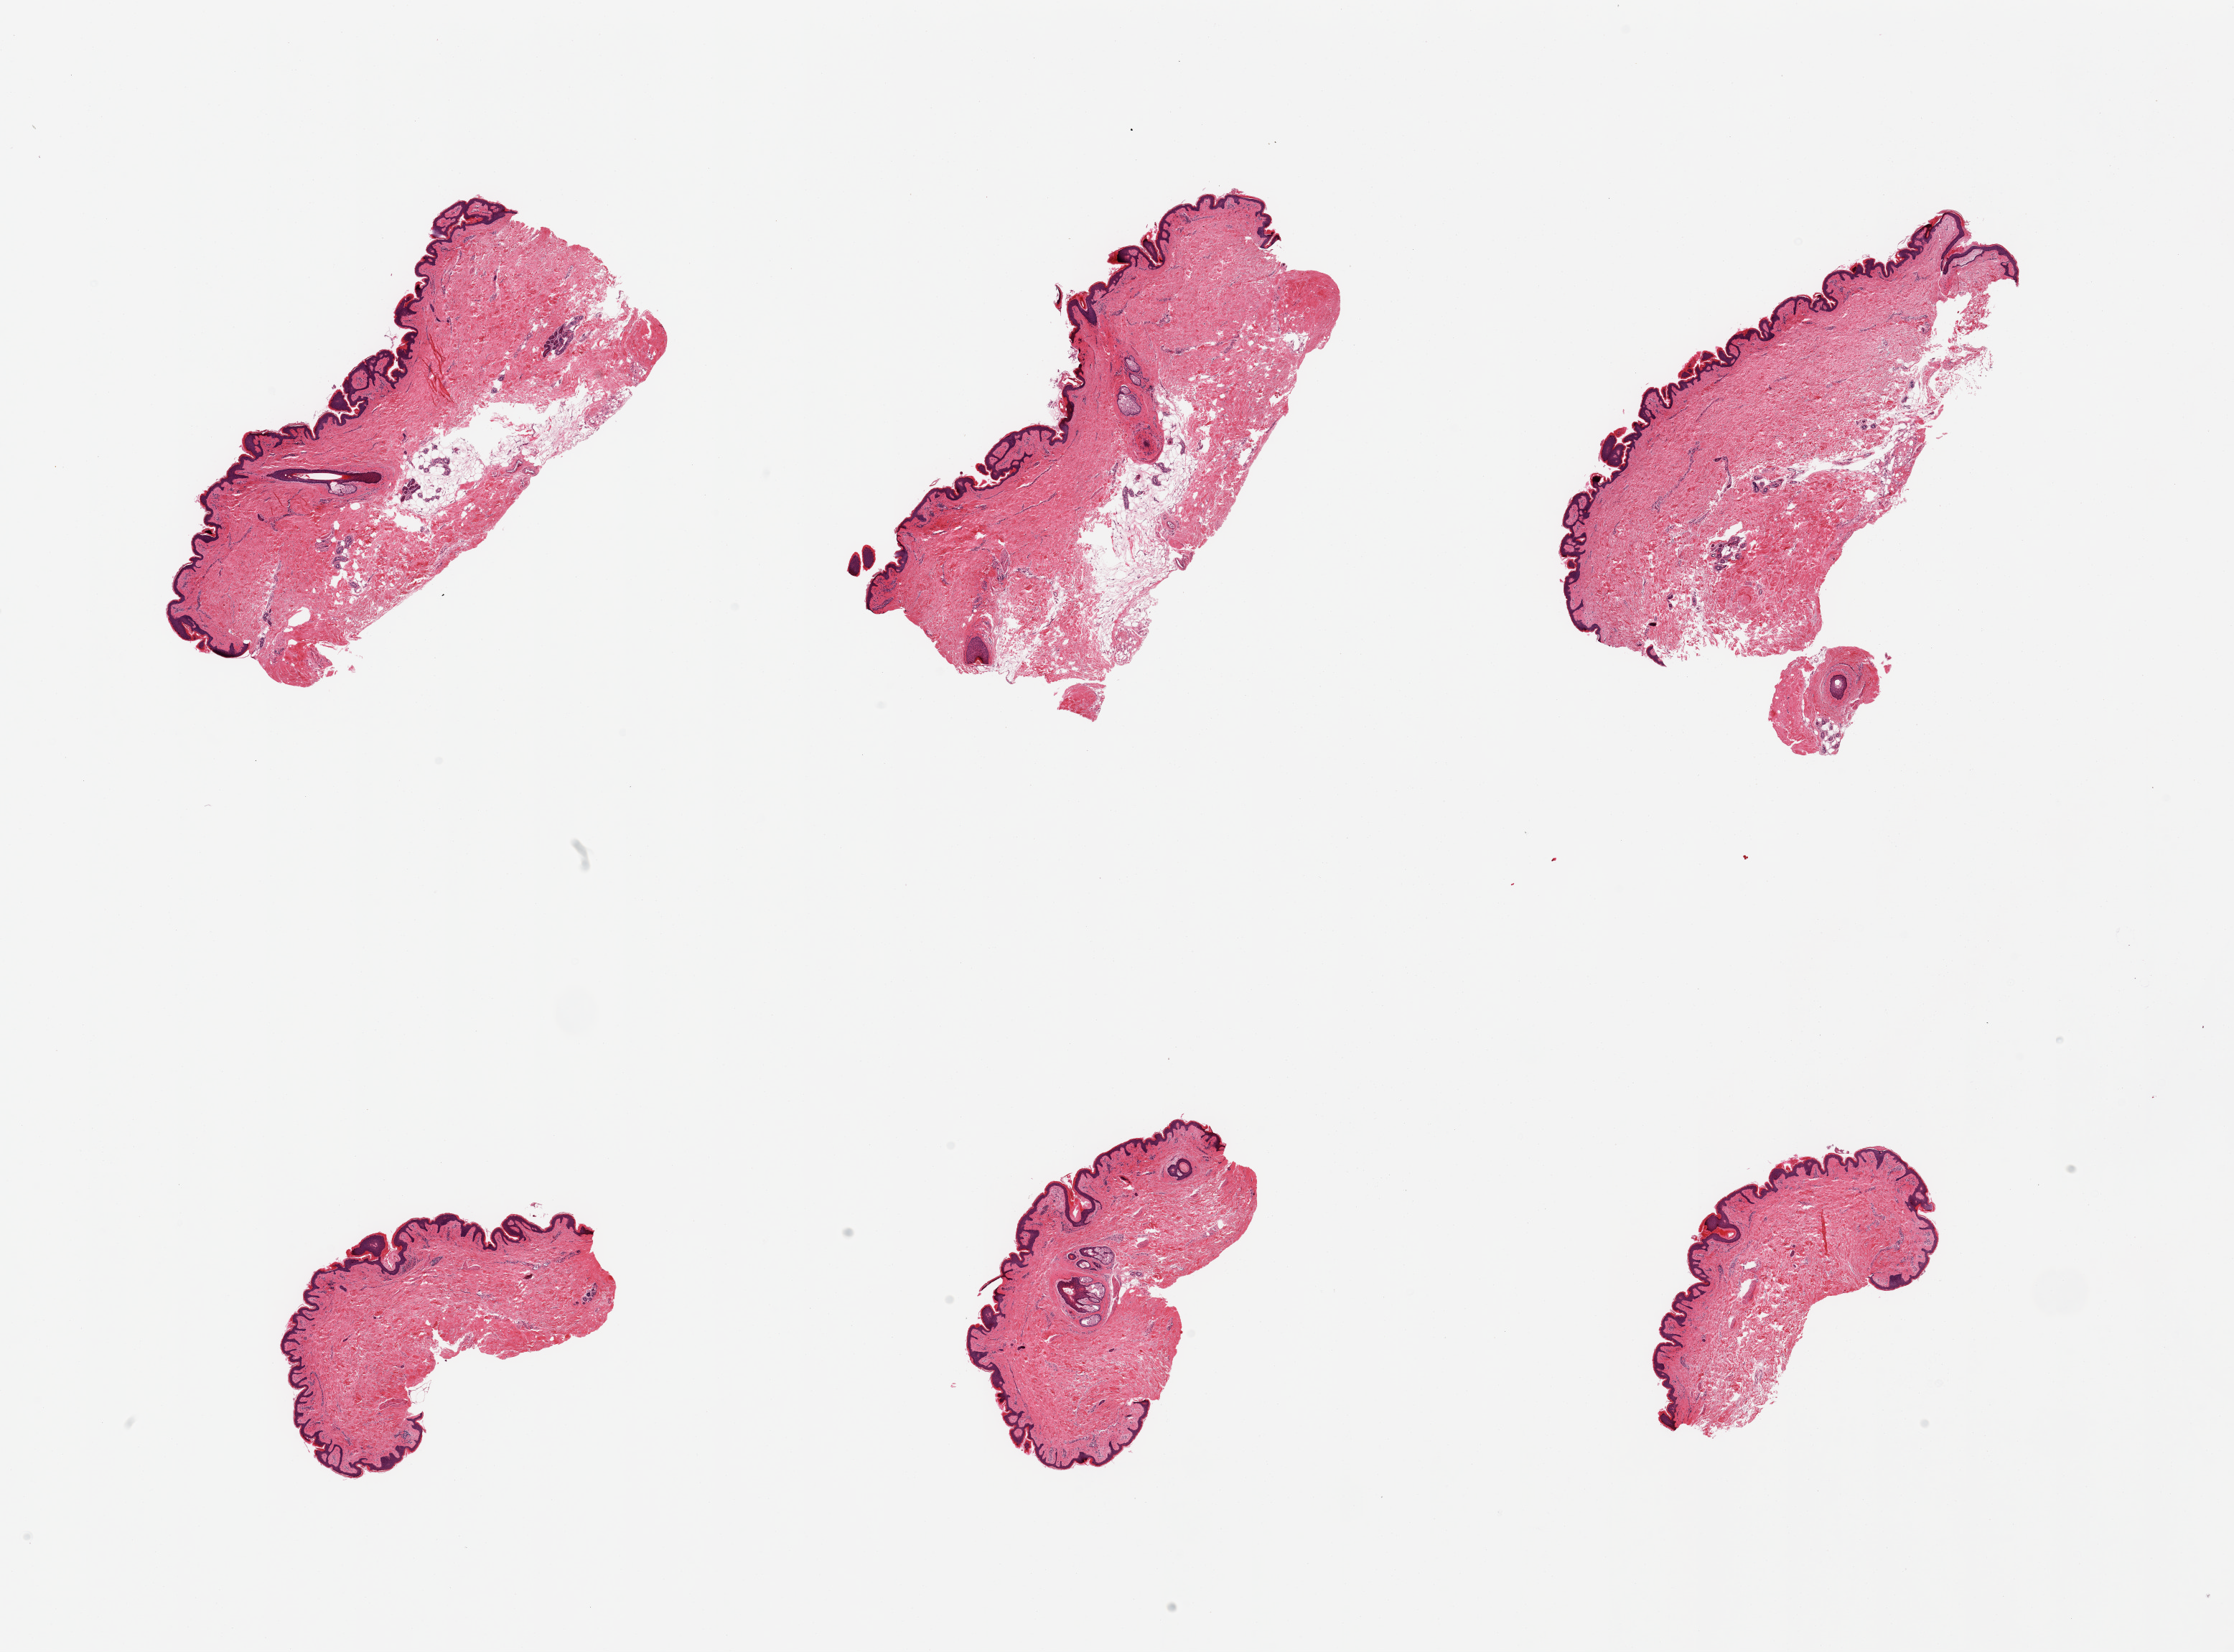
Hematoxylin and eosin (H&E) whole-slide image, brightfield, shown as a low-resolution overview of the whole scanned area (about 24.6 x 18.2 mm). PAXgene-fixed paraffin-embedded (PFPE) section. Section of skin of suprapubic region (target tissue). Tissue donor sample. Male donor.
Review note (as recorded): 6 pieces; 20% dermal fat in the 2 larger pieces.